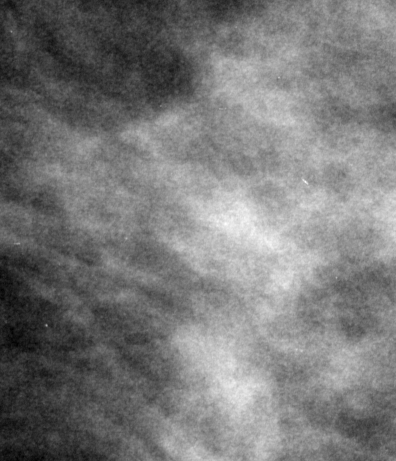
Region of interest cut from a scanned film mammogram (one marked finding), right breast, MLO view, BI-RADS breast density category 3 (scale 1–4).
- Marked abnormality: mass, shape architectural distortion, margins spiculated; BI-RADS assessment category 5; pathology result (as recorded, not read from the image): malignant.